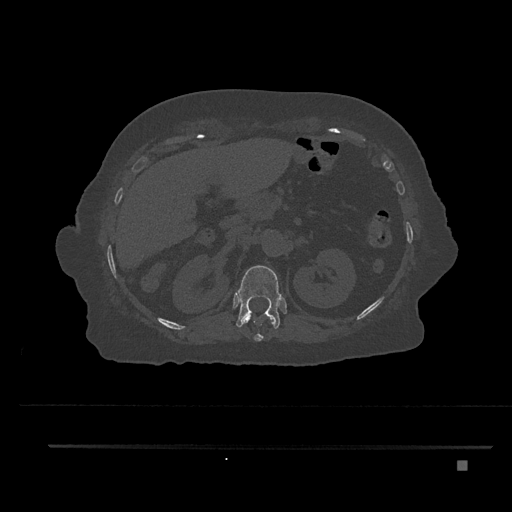
CT including the spine, one axial slice; position 277 of 797 along the scan axis; reconstruction kernel Br40s/3; 120 kVp; bone window (W 1800 / L 400 HU); 0.5 mm slice thickness; 512 × 512 image matrix, field of view 437 × 437 mm. Patient: female, 76 years. From the clinical record (not read from this slice): primary cancer: lung.
Outlined on this slice (semi-automatically segmented with operator editing):
- T11 vertebra: bounding box <242,313,274,341> (left, top, right, bottom; pixels)
- T12 vertebra: <235,265,282,329>